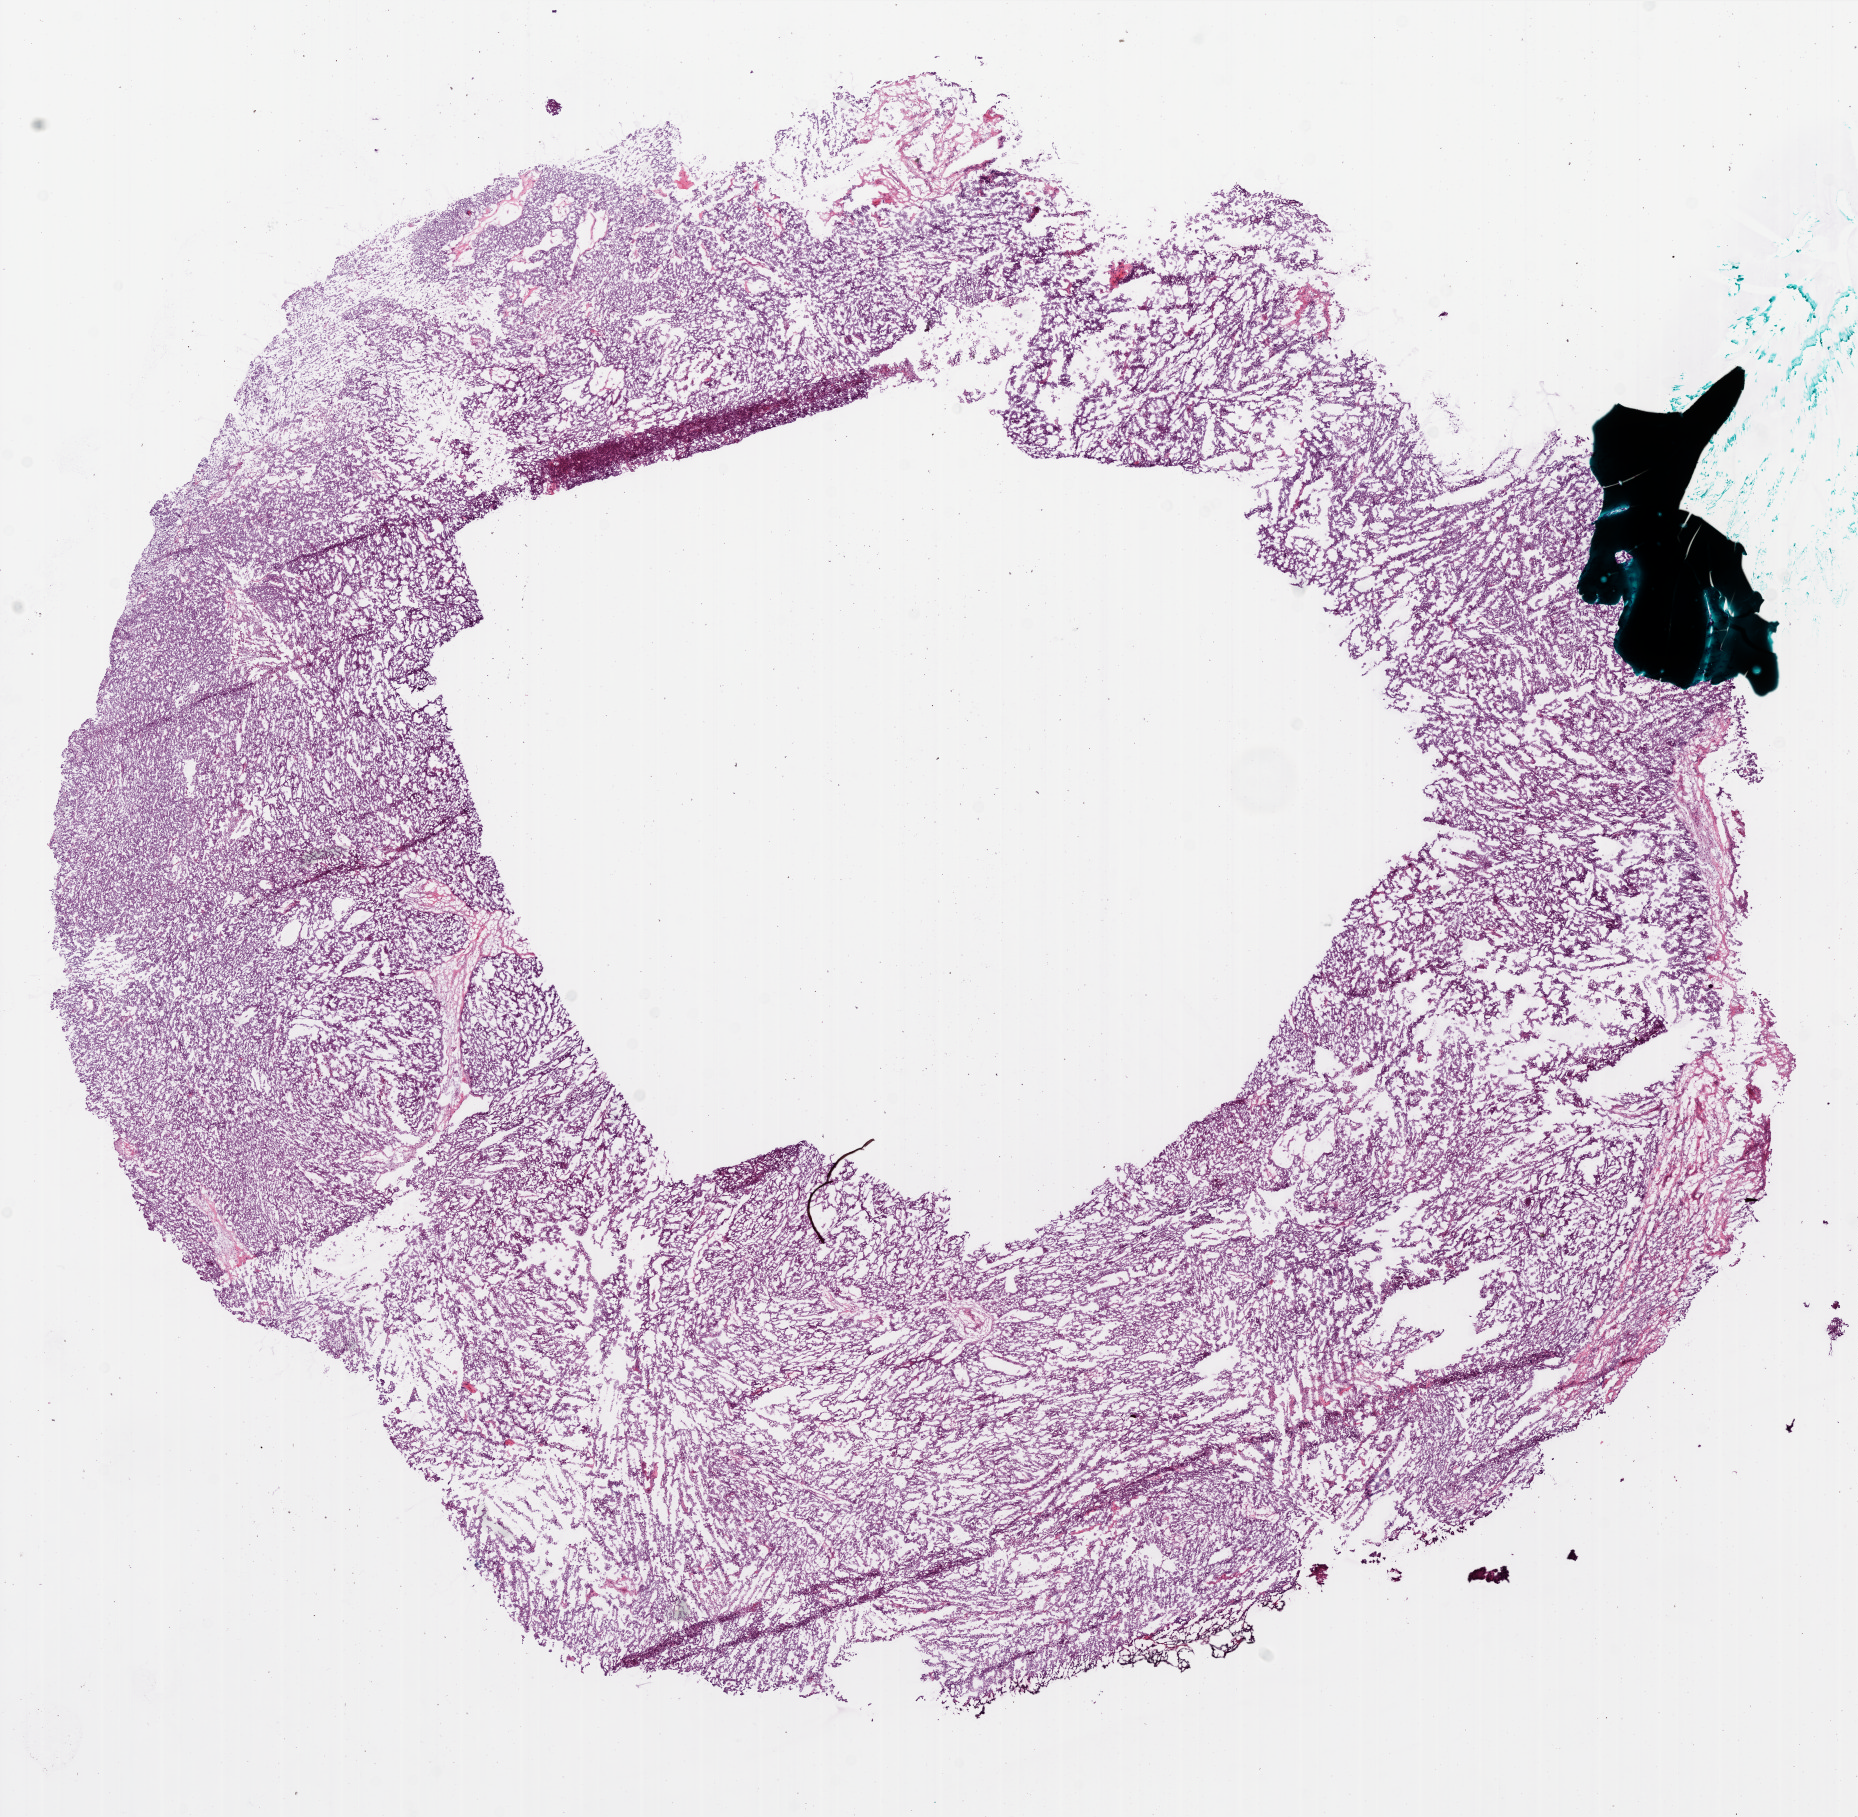
H&E whole-slide image — whole scanned area (about 14.9 x 14.6 mm, slide scanned at 20x) shown as a low-resolution overview; frozen section from the bottom of the tissue portion; primary tumour sample from the ovary. Patient: female, age at initial diagnosis 73 years. Histologic grade: G3 (poorly differentiated). Composition of this section per pathologist review: tumour cells 95%, tumour nuclei 98%, normal cells 0%, stromal cells 4%, necrosis 1%.
FIGO stage: IIIC. Laterality: bilateral. Pathologic diagnosis: Serous cystadenocarcinoma, NOS.